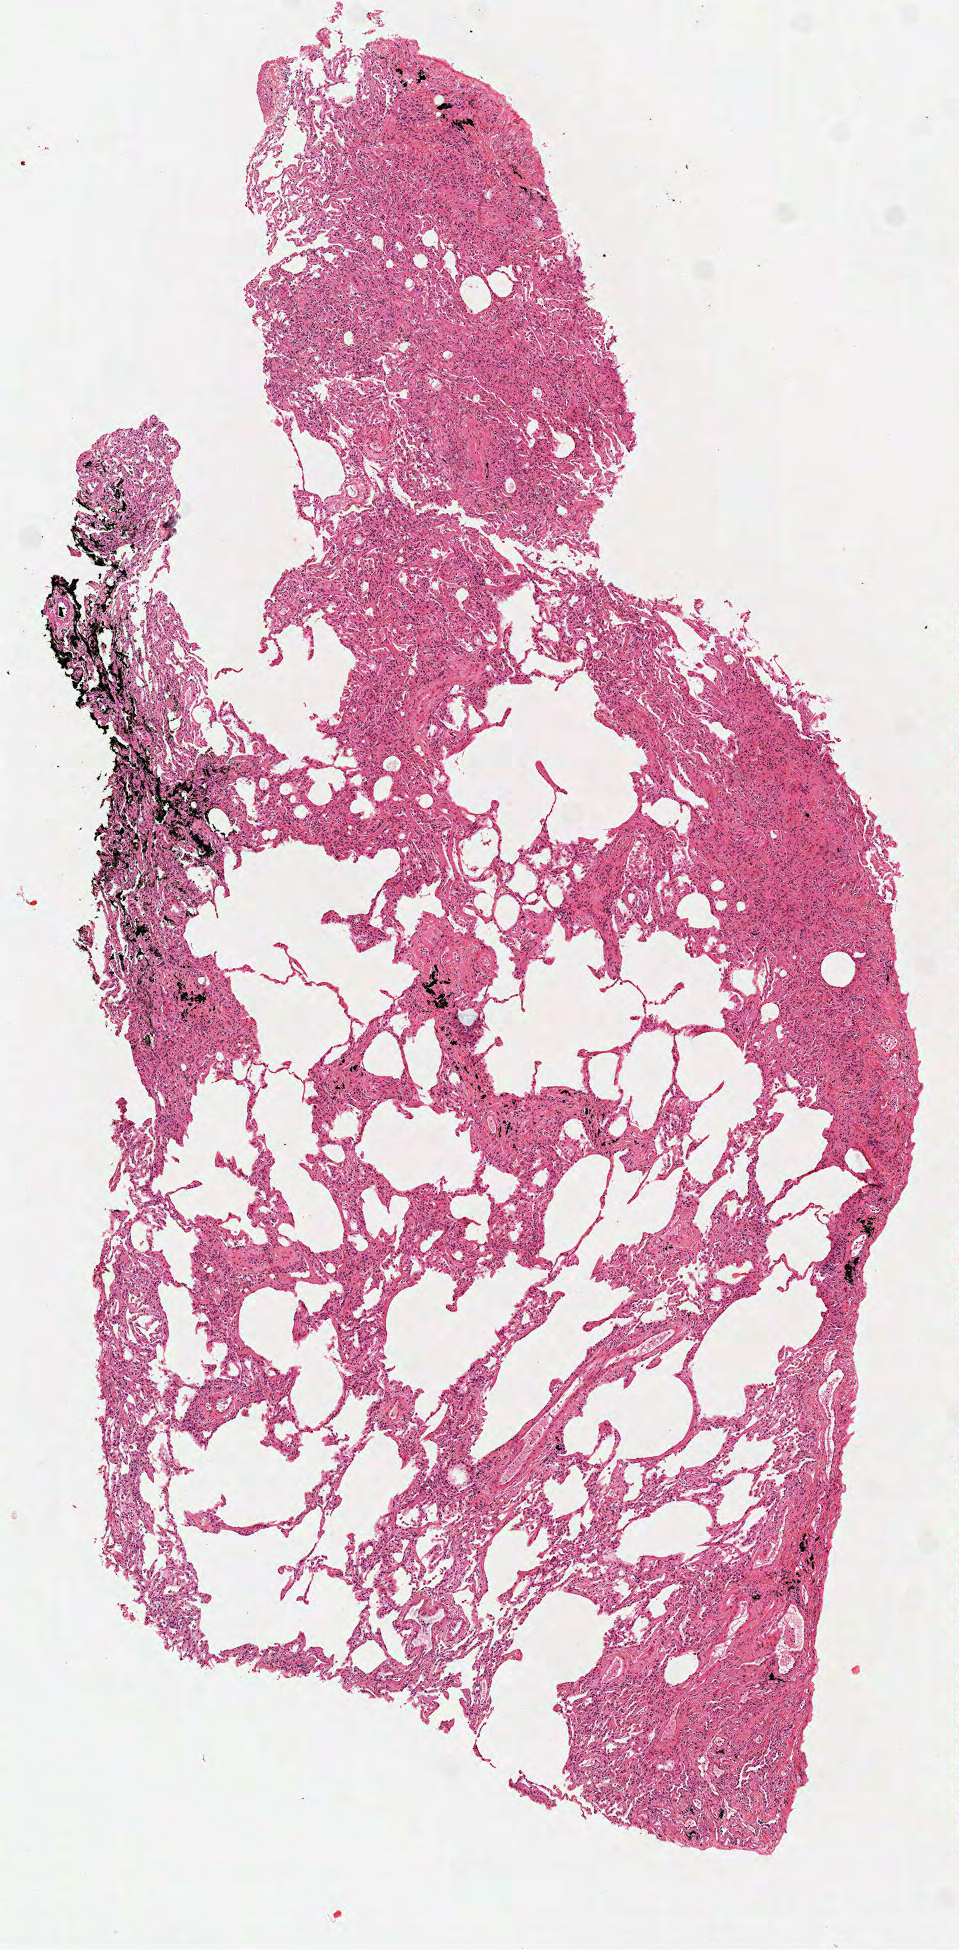
Digitized H&E tissue section (whole slide), a low-resolution overview of the entire scanned area, about 3.9 x 7.9 mm (from a 40x scan), frozen section, sample: solid tissue normal (non-tumour tissue), lung. Male patient; age at initial diagnosis 67 years.
* this section: solid tissue normal sample (biorepository sample class)
* patient diagnosis: Squamous cell carcinoma, NOS